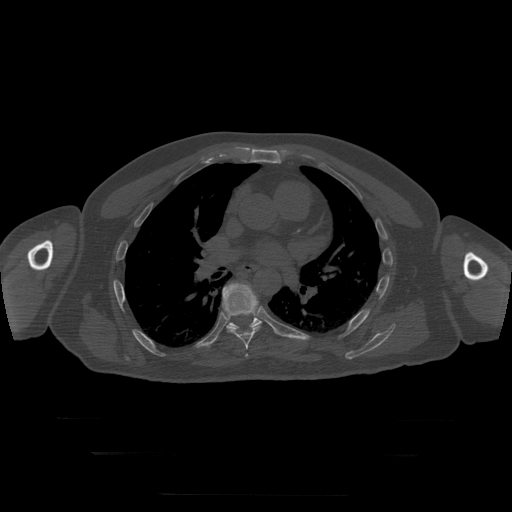
CT including the spine, one axial slice. Slice 179 of 397 in the series (ordered by position). Reconstruction kernel STANDARD. 120 kVp. Bone window (W 1800 / L 400 HU). 1.25 mm slice thickness. 512 × 512 image matrix, field of view 510 × 510 mm. Patient age 73 years. From the clinical record (not read from this slice): primary cancer: prostate.
Annotated regions visible in this slice (semi-automatically segmented with operator editing):
- T6 vertebra: box from (x=245, y=354) to (x=249, y=357) px
- T7 vertebra: (x=222, y=283)–(x=260, y=350)
- T8 vertebra: (x=227, y=318)–(x=262, y=330)